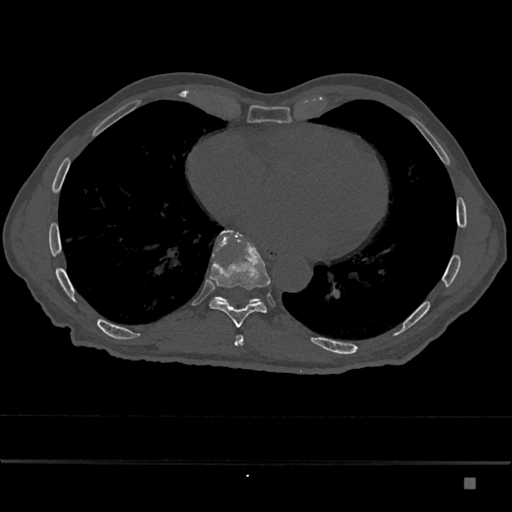
CT including the spine, one axial slice. Position 792 of 797 along the scan axis. Bone window (W 1800 / L 400 HU). 0.5 mm slice thickness. 512 × 512 image matrix, field of view 390 × 390 mm. Male patient, age 72 years. Case-level facts recorded for this patient, not image findings: primary cancer: prostate.
Outlined on this slice (semi-automatically segmented with operator editing):
- T10 vertebra: bounding box [x1, y1, x2, y2] px = [214, 230, 261, 303]
- T9 vertebra: [209, 230, 271, 328]